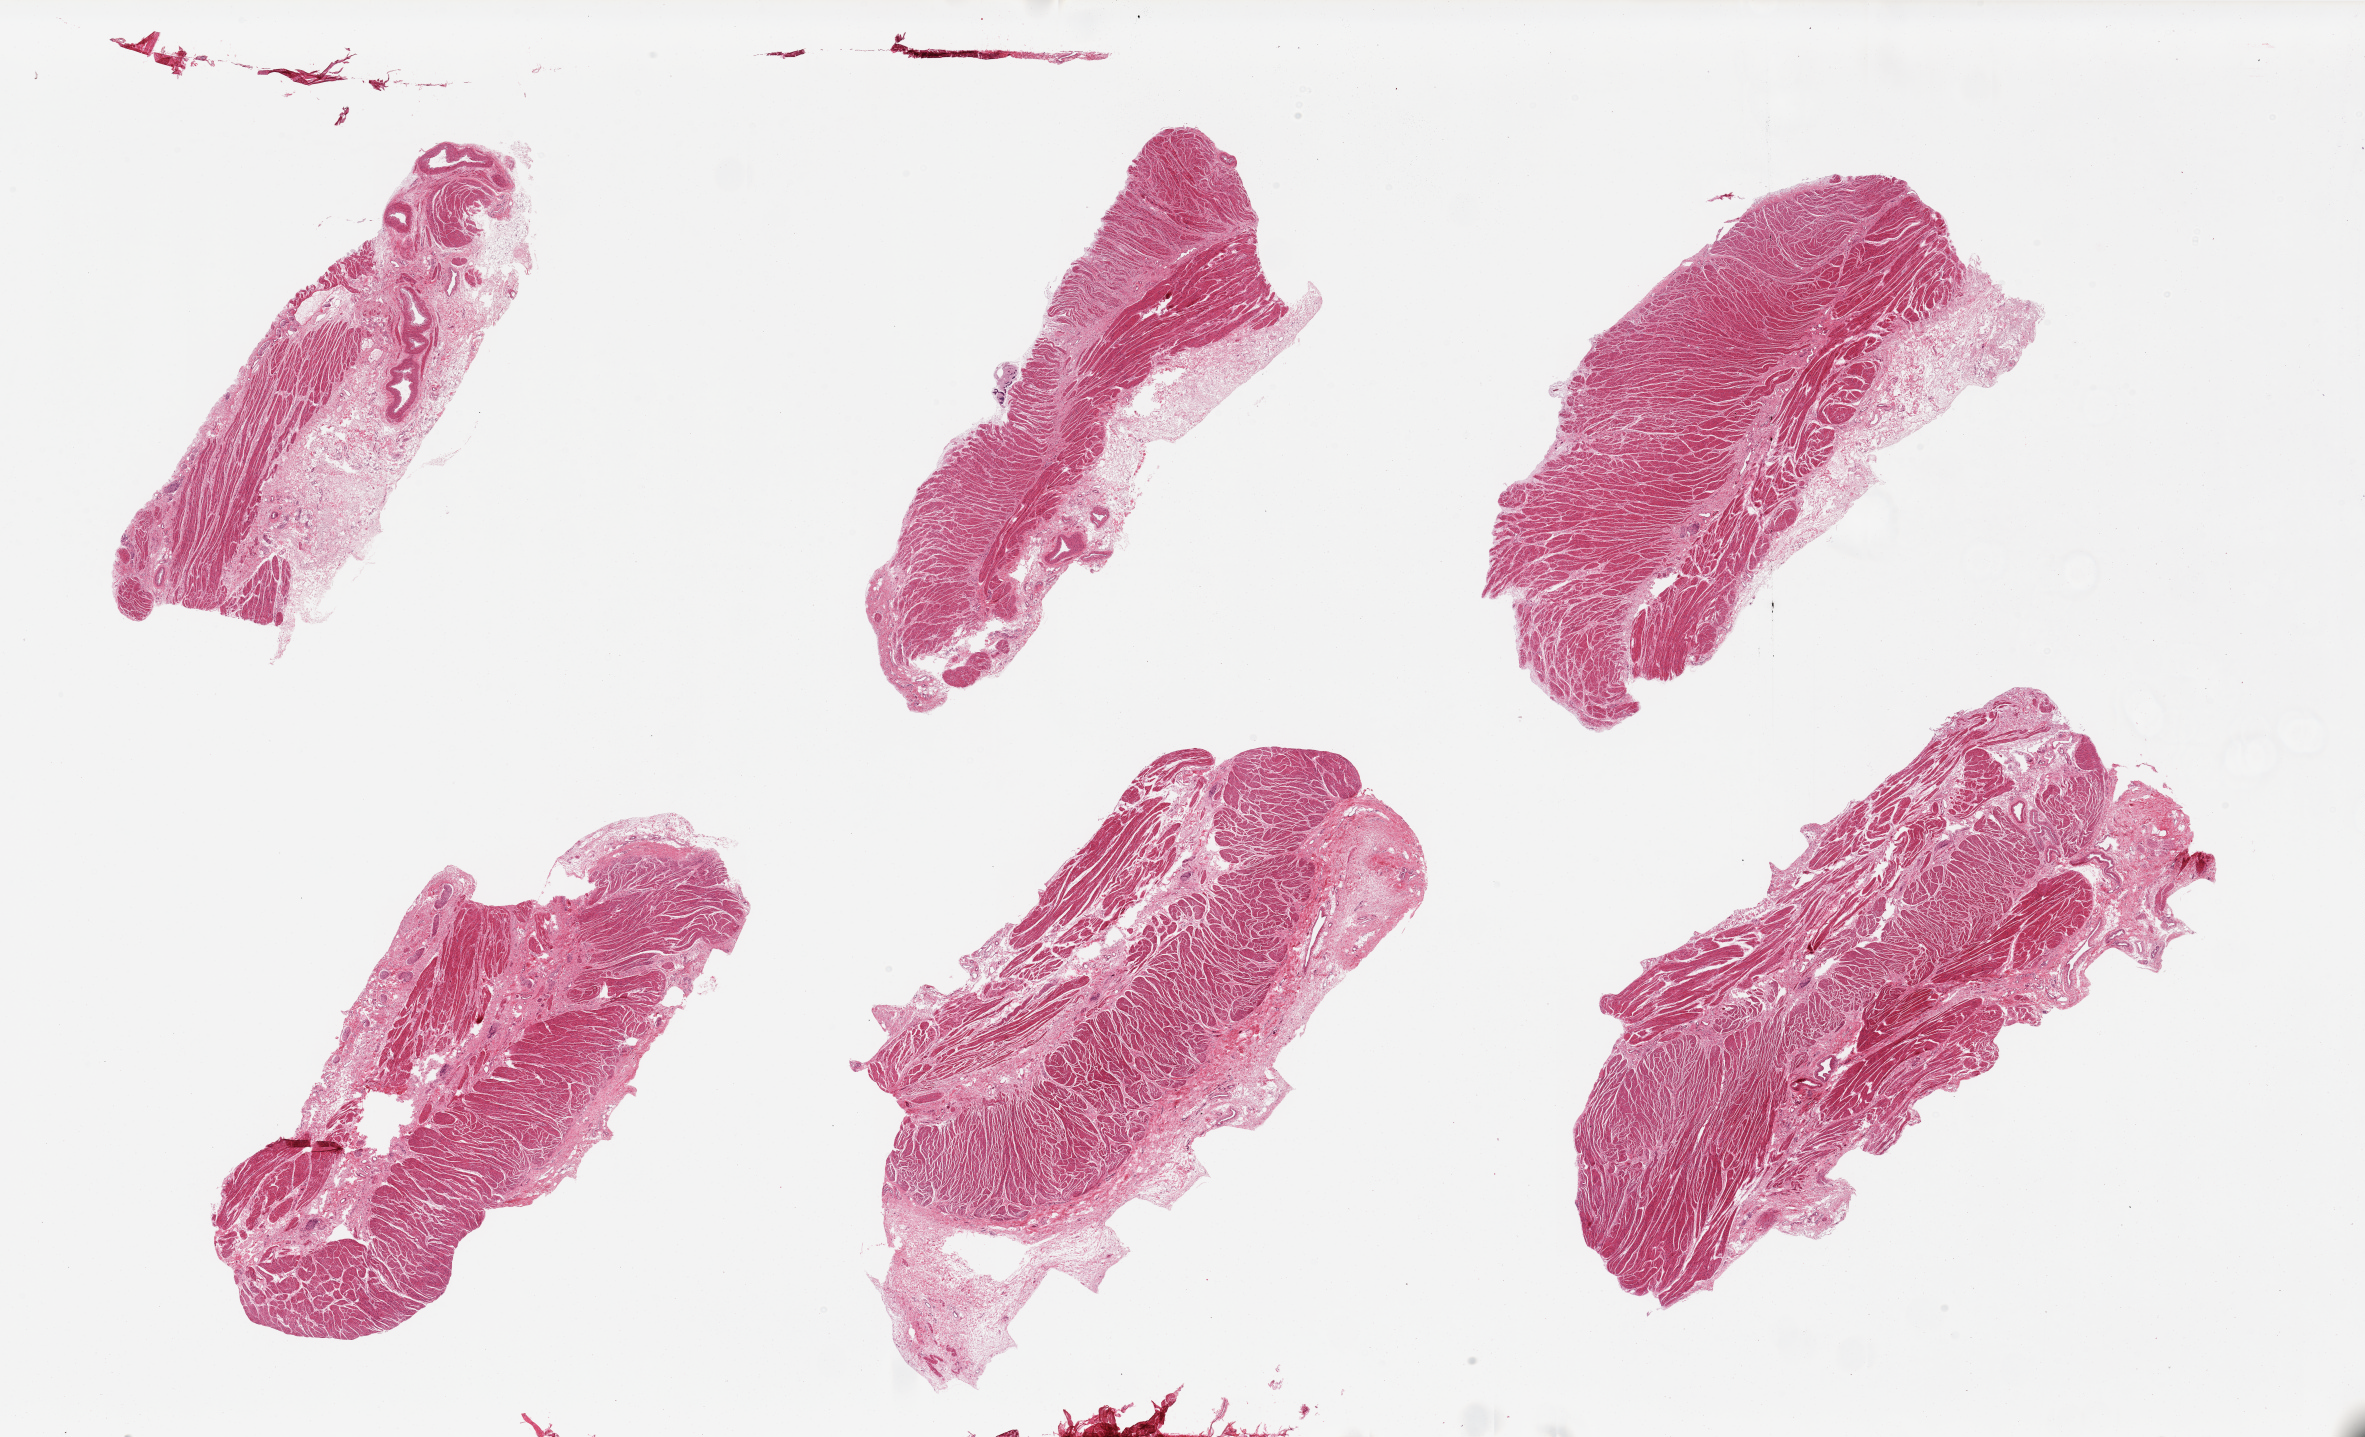
Whole-slide image, hematoxylin and eosin (H&E) stain, a low-resolution overview of the entire scanned area, about 37.4 x 22.7 mm (from a 20x scan), PAXgene-fixed paraffin-embedded (PFPE) section, target tissue: gastroesophageal junction, tissue donor sample. Donor: female.
Reviewer comment on this tissue sample: 6 pieces, no residual mucosa.